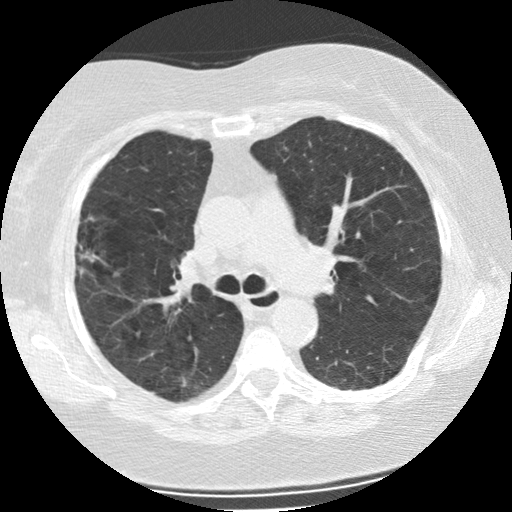
Chest CT (low-dose screening protocol), one axial image; second screening round (one year after baseline); lung window (W 1500 / L -600 HU); 2.5 mm slice thickness; slice 78 of 225 in the series; 512 × 512 image matrix. Female, age 73 years at enrolment. Former smoker at enrolment.
- Expert-annotated lung lesion, bounding box (x1, y1, x2, y2) in pixels: (53, 220, 114, 290).
- The screening reader recorded 2 non-calcified nodules or masses ≥4 mm on this exam (right upper lobe, left upper lobe); which of them this box marks is not recorded.
- Participant outcome: lung cancer diagnosed 47 days after this screen — bronchiolo-alveolar adenocarcinoma, NOS, right upper lobe, moderately differentiated (G2), stage IIIB (AJCC 6th edition), 21 mm at pathology.